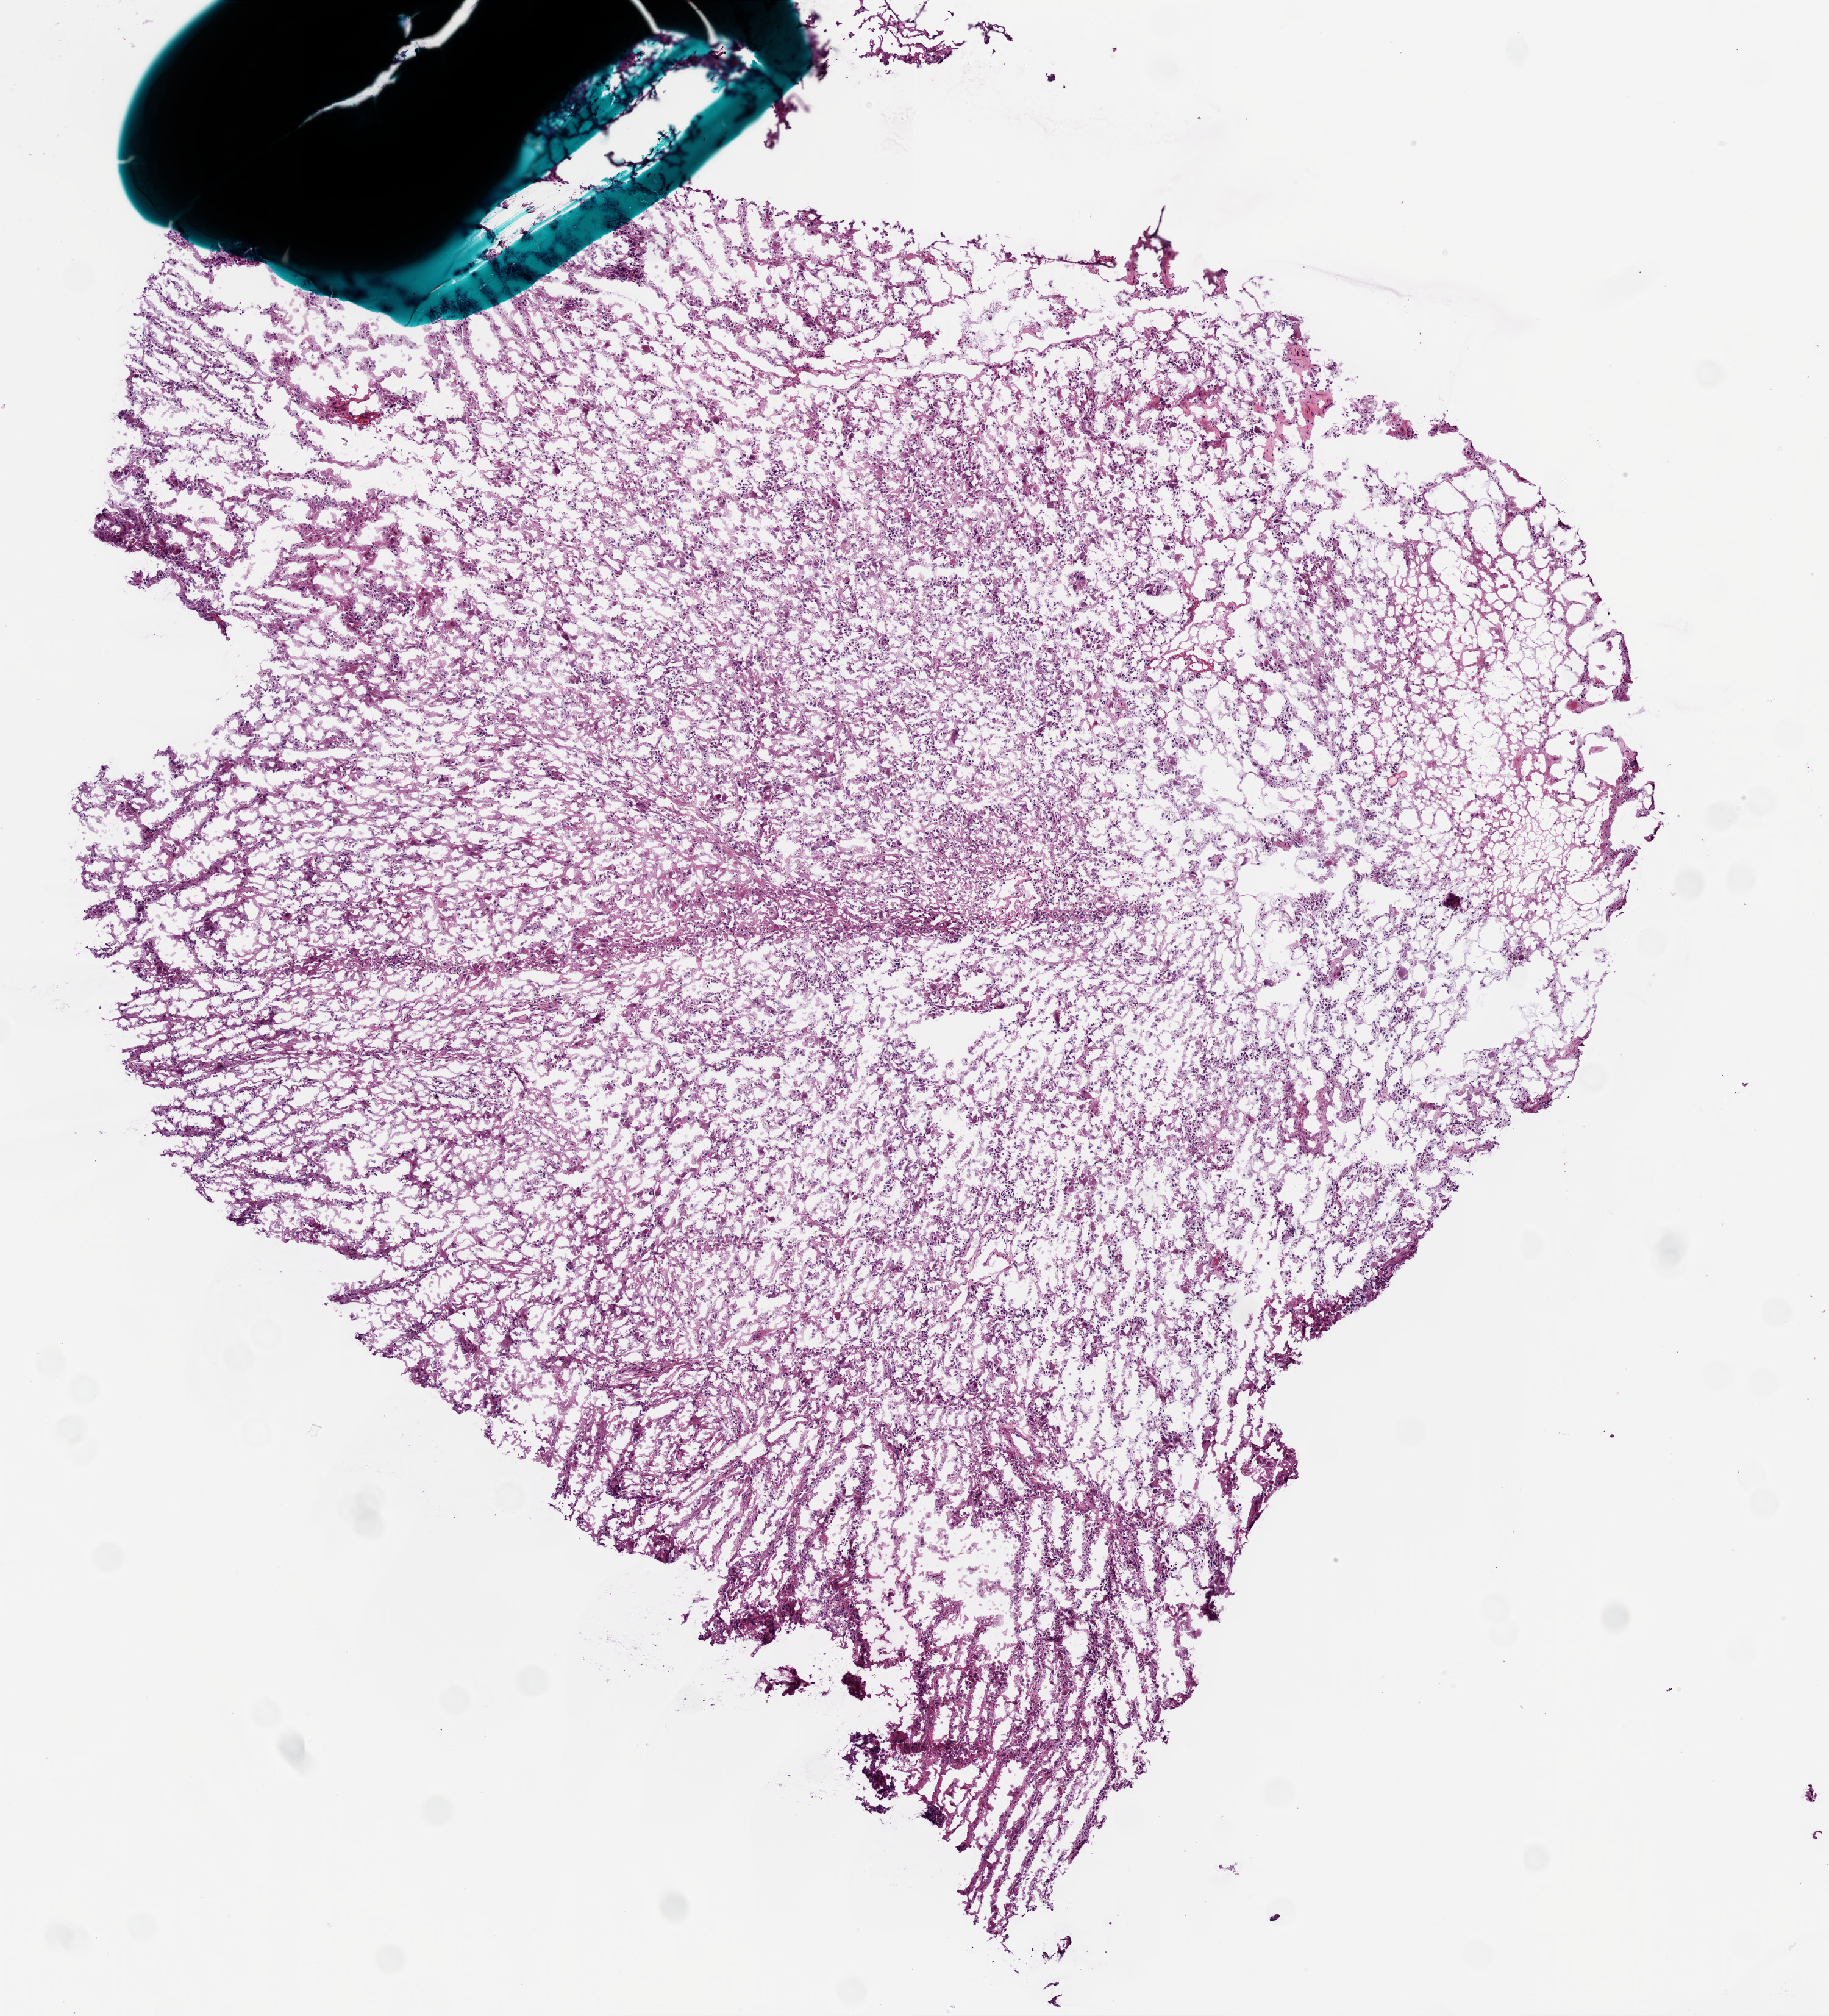
Whole-slide histology image, Hematoxylin and eosin (H&E) stained — whole scanned area (about 6.0 x 6.6 mm, acquisition: 20x scan) shown as a low-resolution overview; frozen section; brain, primary tumour sample. Male patient; age at initial diagnosis 36 years. Slide review estimates, as recorded: tumour cells 85%, tumour nuclei 80%, normal cells 15%, stromal cells 5%, necrosis 0%.
Diagnosis: Glioblastoma.